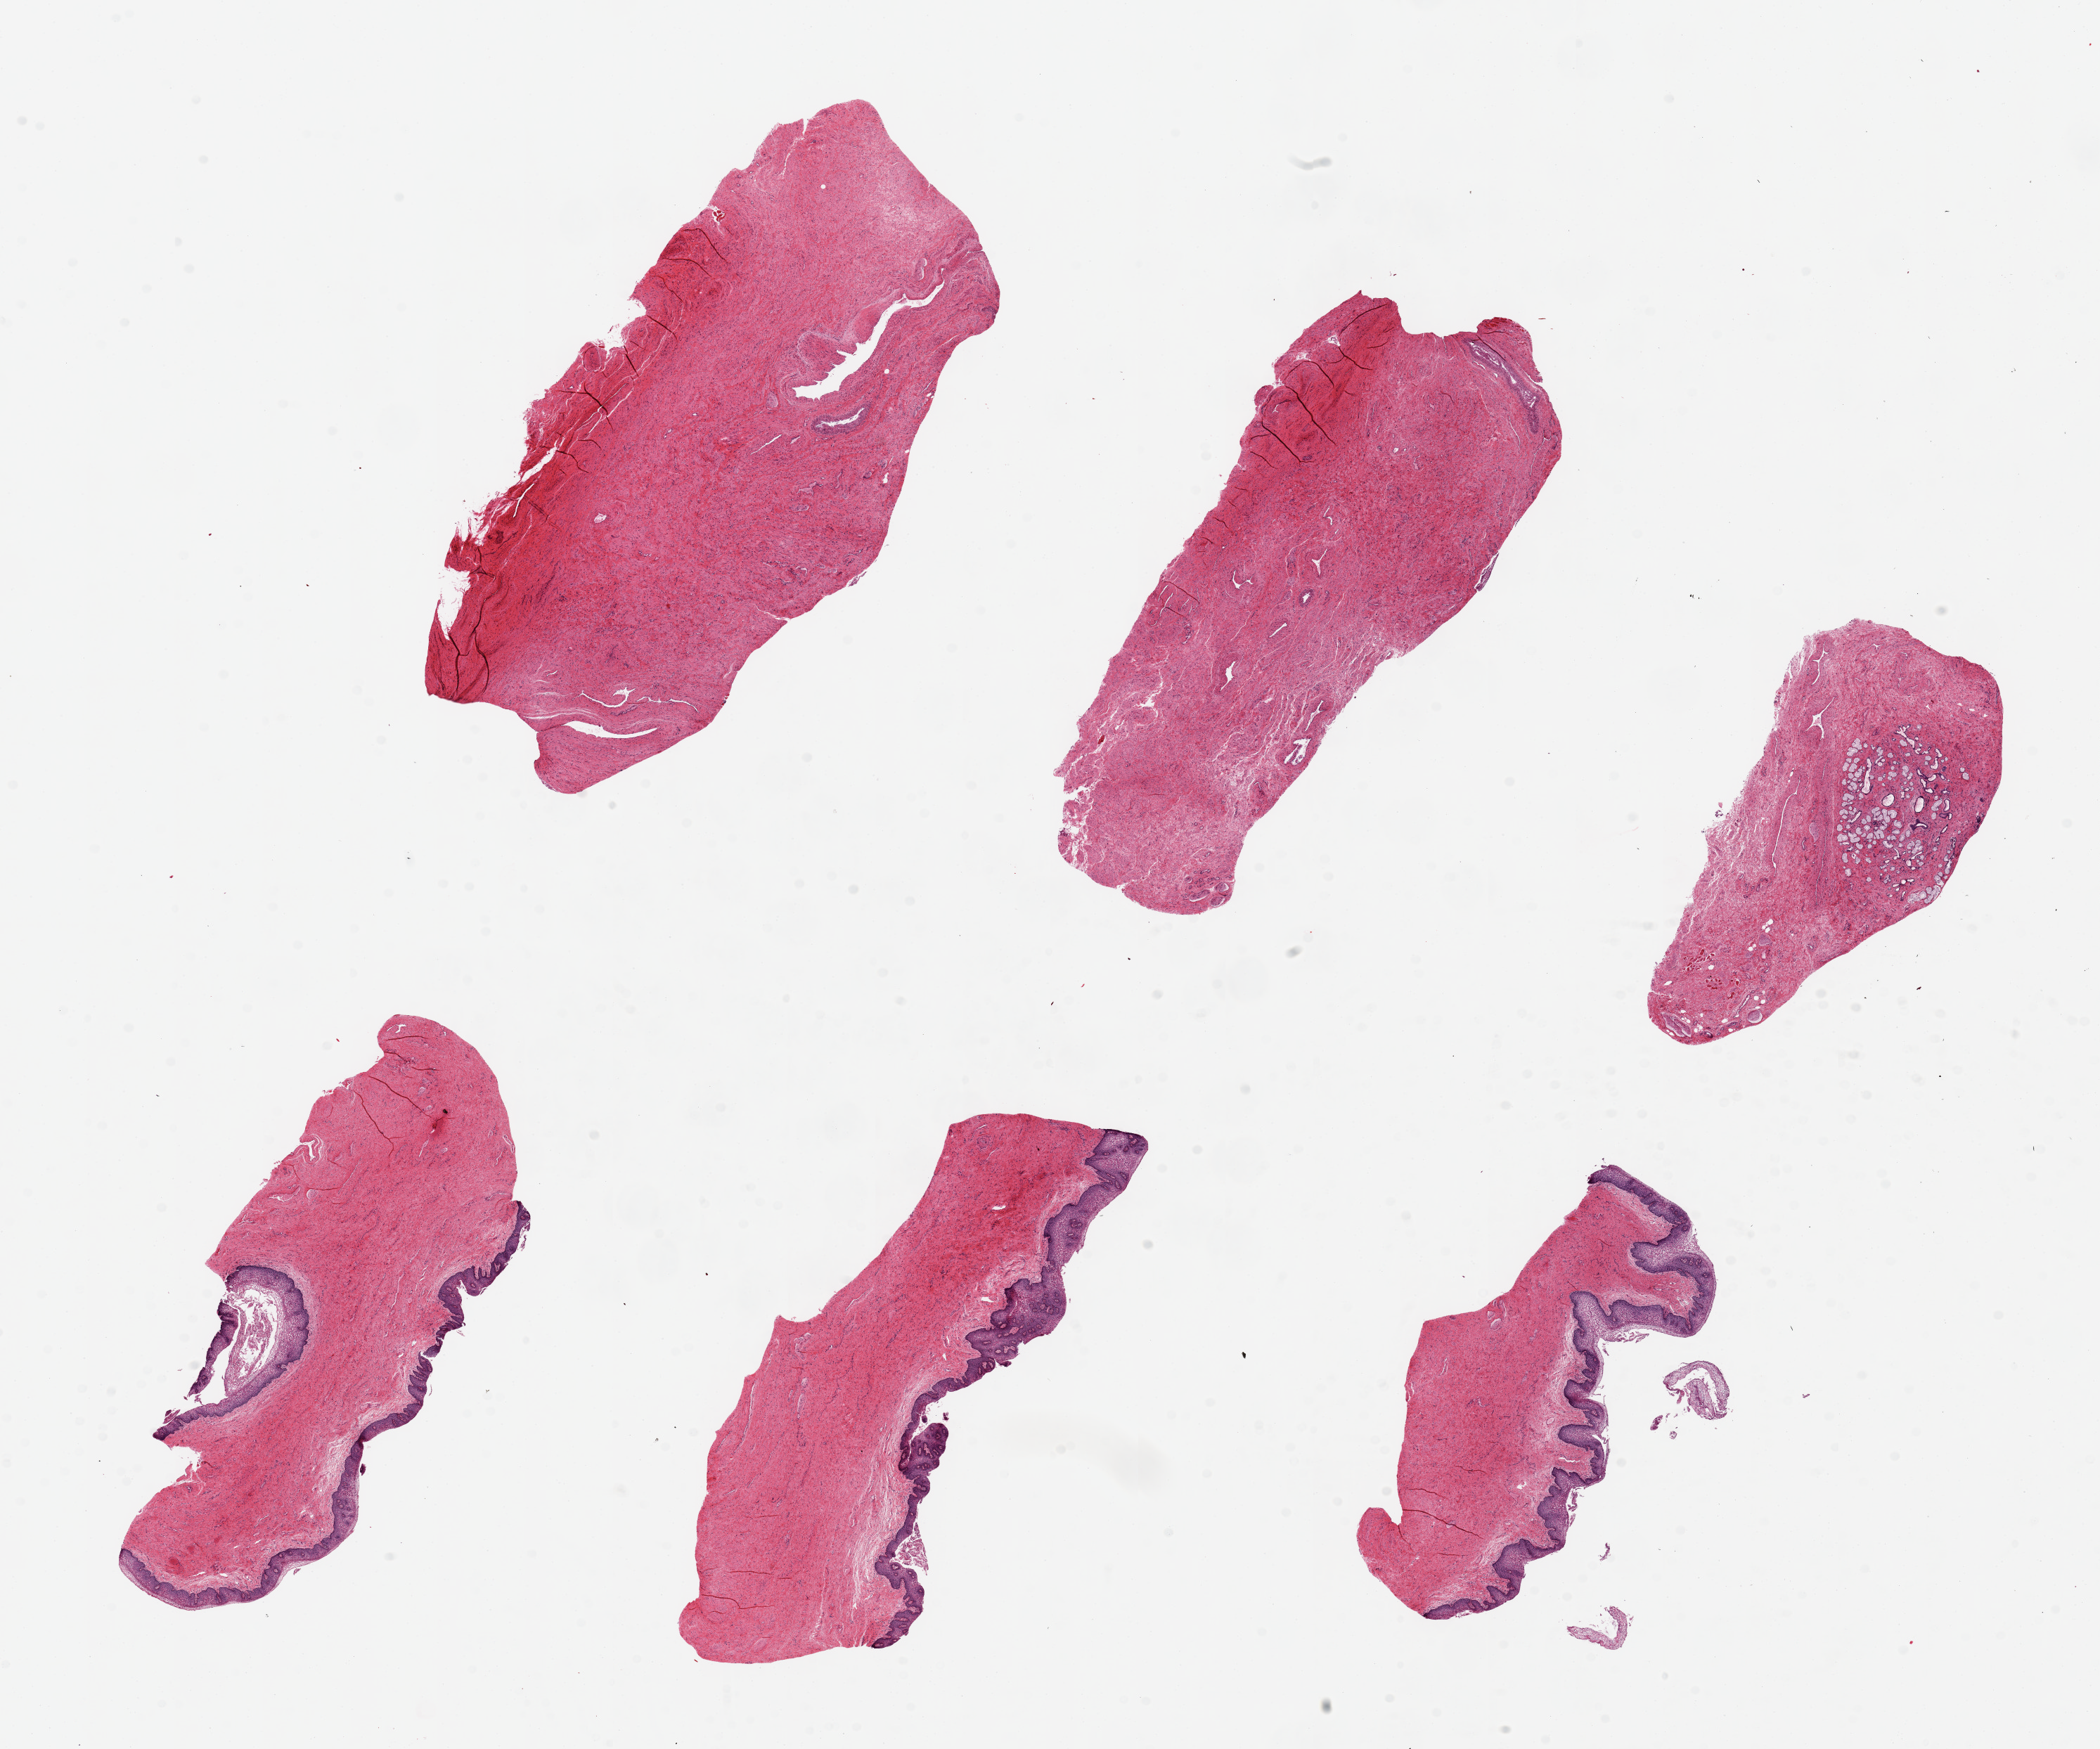
Whole-slide image, hematoxylin and eosin (H&E) stain — a low-resolution overview of the entire scanned area, about 23.6 x 19.7 mm (from a 20x scan). PAXgene-fixed, paraffin-embedded tissue. Section of vagina (target tissue). Donor tissue sample. Donor: female.
Review note (as recorded): 6 pieces ~6x2.5mm 50% with squamous mucosa ~10-15% thickness; Focal mesonephric duct remnants in one aliquot.